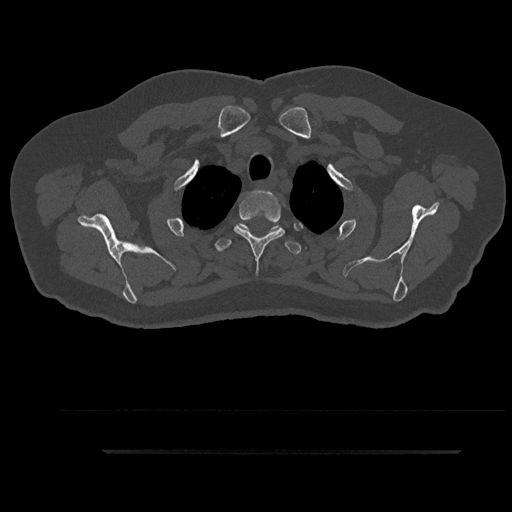
CT including the spine, one axial slice; slice 750 of 797 in the series (ordered by position); reconstruction kernel Br40s/3; 120 kVp; bone window (W 1800 / L 400 HU); 0.5 mm slice thickness; 512 × 512 image matrix, field of view 432 × 432 mm. Patient: male, 63 years. Case-level facts recorded for this patient, not image findings: primary cancer: renal; vertebrae with lytic lesions (as recorded): T8.
Outlined on this slice (semi-automatically segmented with operator editing):
- T2 vertebra: bounding box [x1, y1, x2, y2] px = [234, 191, 302, 274]
- T3 vertebra: [215, 222, 302, 255]